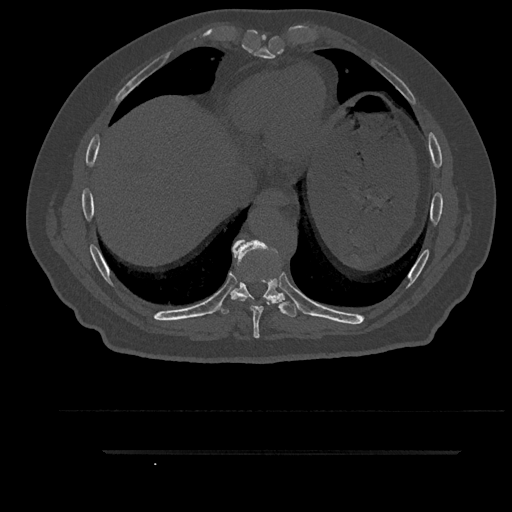
CT including the spine, one axial slice; position 447 of 797 along the scan axis; reconstruction kernel Br40s/3; 120 kVp; bone window (W 1800 / L 400 HU); 0.5 mm slice thickness; 512 × 512 image matrix, field of view 432 × 432 mm. Male patient, age 63 years. From the clinical record (not read from this slice): primary cancer: renal.
Outlined on this slice (semi-automatically segmented with operator editing):
- T10 vertebra: bounding box <281,293,285,297> (left, top, right, bottom; pixels)
- T8 vertebra: <231,239,279,339>
- T9 vertebra: <215,252,297,318>